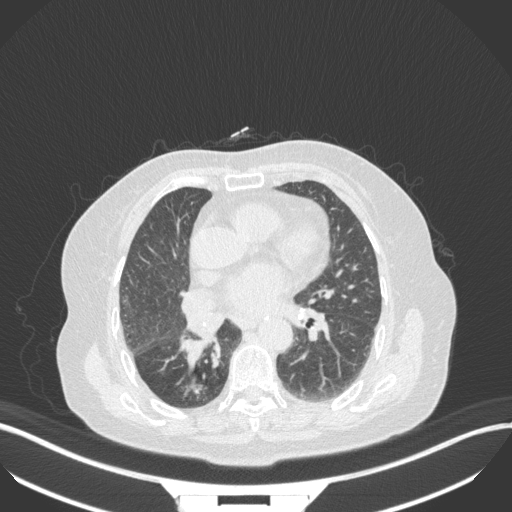
Chest CT, one axial slice. Slice 151 of 329 in the series (ordered by position). Reconstruction kernel B31f. Lung window (W 1500 / L -600 HU). 1 mm slice thickness. 512 × 512 image matrix, field of view 400 × 400 mm. Patient: female, 75 years. From the clinical record (not read from this slice): clinical TNM (as recorded): T1b N0 M1a.
Outlined on this slice (rectangle marked by the reading radiologist):
- lung tumour (recorded histology: squamous cell carcinoma): box from (x=182, y=334) to (x=214, y=377) px